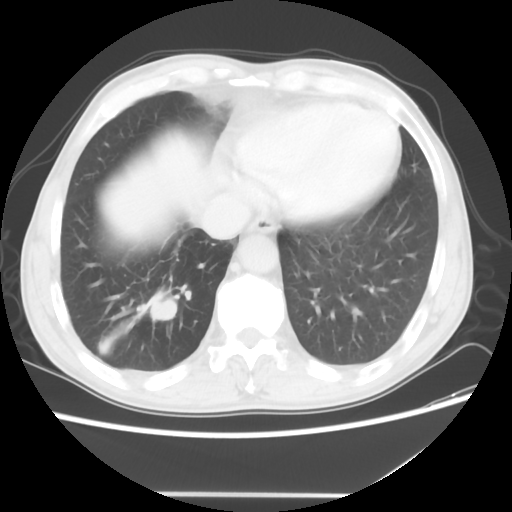
Chest CT, one axial slice. Position 13 of 56 along the scan axis. 120 kVp. Lung window (W 1500 / L -600 HU). 512 × 512 image matrix, field of view 344 × 344 mm. Male patient, age 65 years. From the clinical record (not read from this slice): clinical TNM (as recorded): T1c N3 M0.
Outlined on this slice (bounding box drawn by a radiologist):
- lung tumour (recorded histology: small cell carcinoma): bounding box [x1, y1, x2, y2] px = [136, 286, 184, 323]